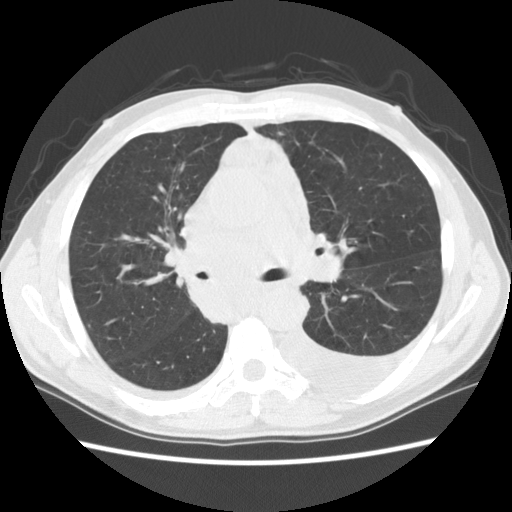
Chest CT (low-dose screening protocol), one axial image, first (baseline) screen, lung window (W 1500 / L -600 HU), 2.5 mm slice thickness, standard (soft-tissue) reconstruction kernel (STANDARD), 140 kVp. Male, age 60 years at enrolment. Current smoker at enrolment.
Lesion marked by an expert reader, box from (x=177, y=237) to (x=295, y=327) px. Screening reader's record for this exam: no non-calcified nodule ≥4 mm recorded. Official screen result: negative screen, significant abnormalities not suspicious for lung cancer. Lung cancer was diagnosed 12 days after this screen: squamous cell carcinoma, NOS, carina, poorly differentiated (G3), stage IV (AJCC 6th edition).